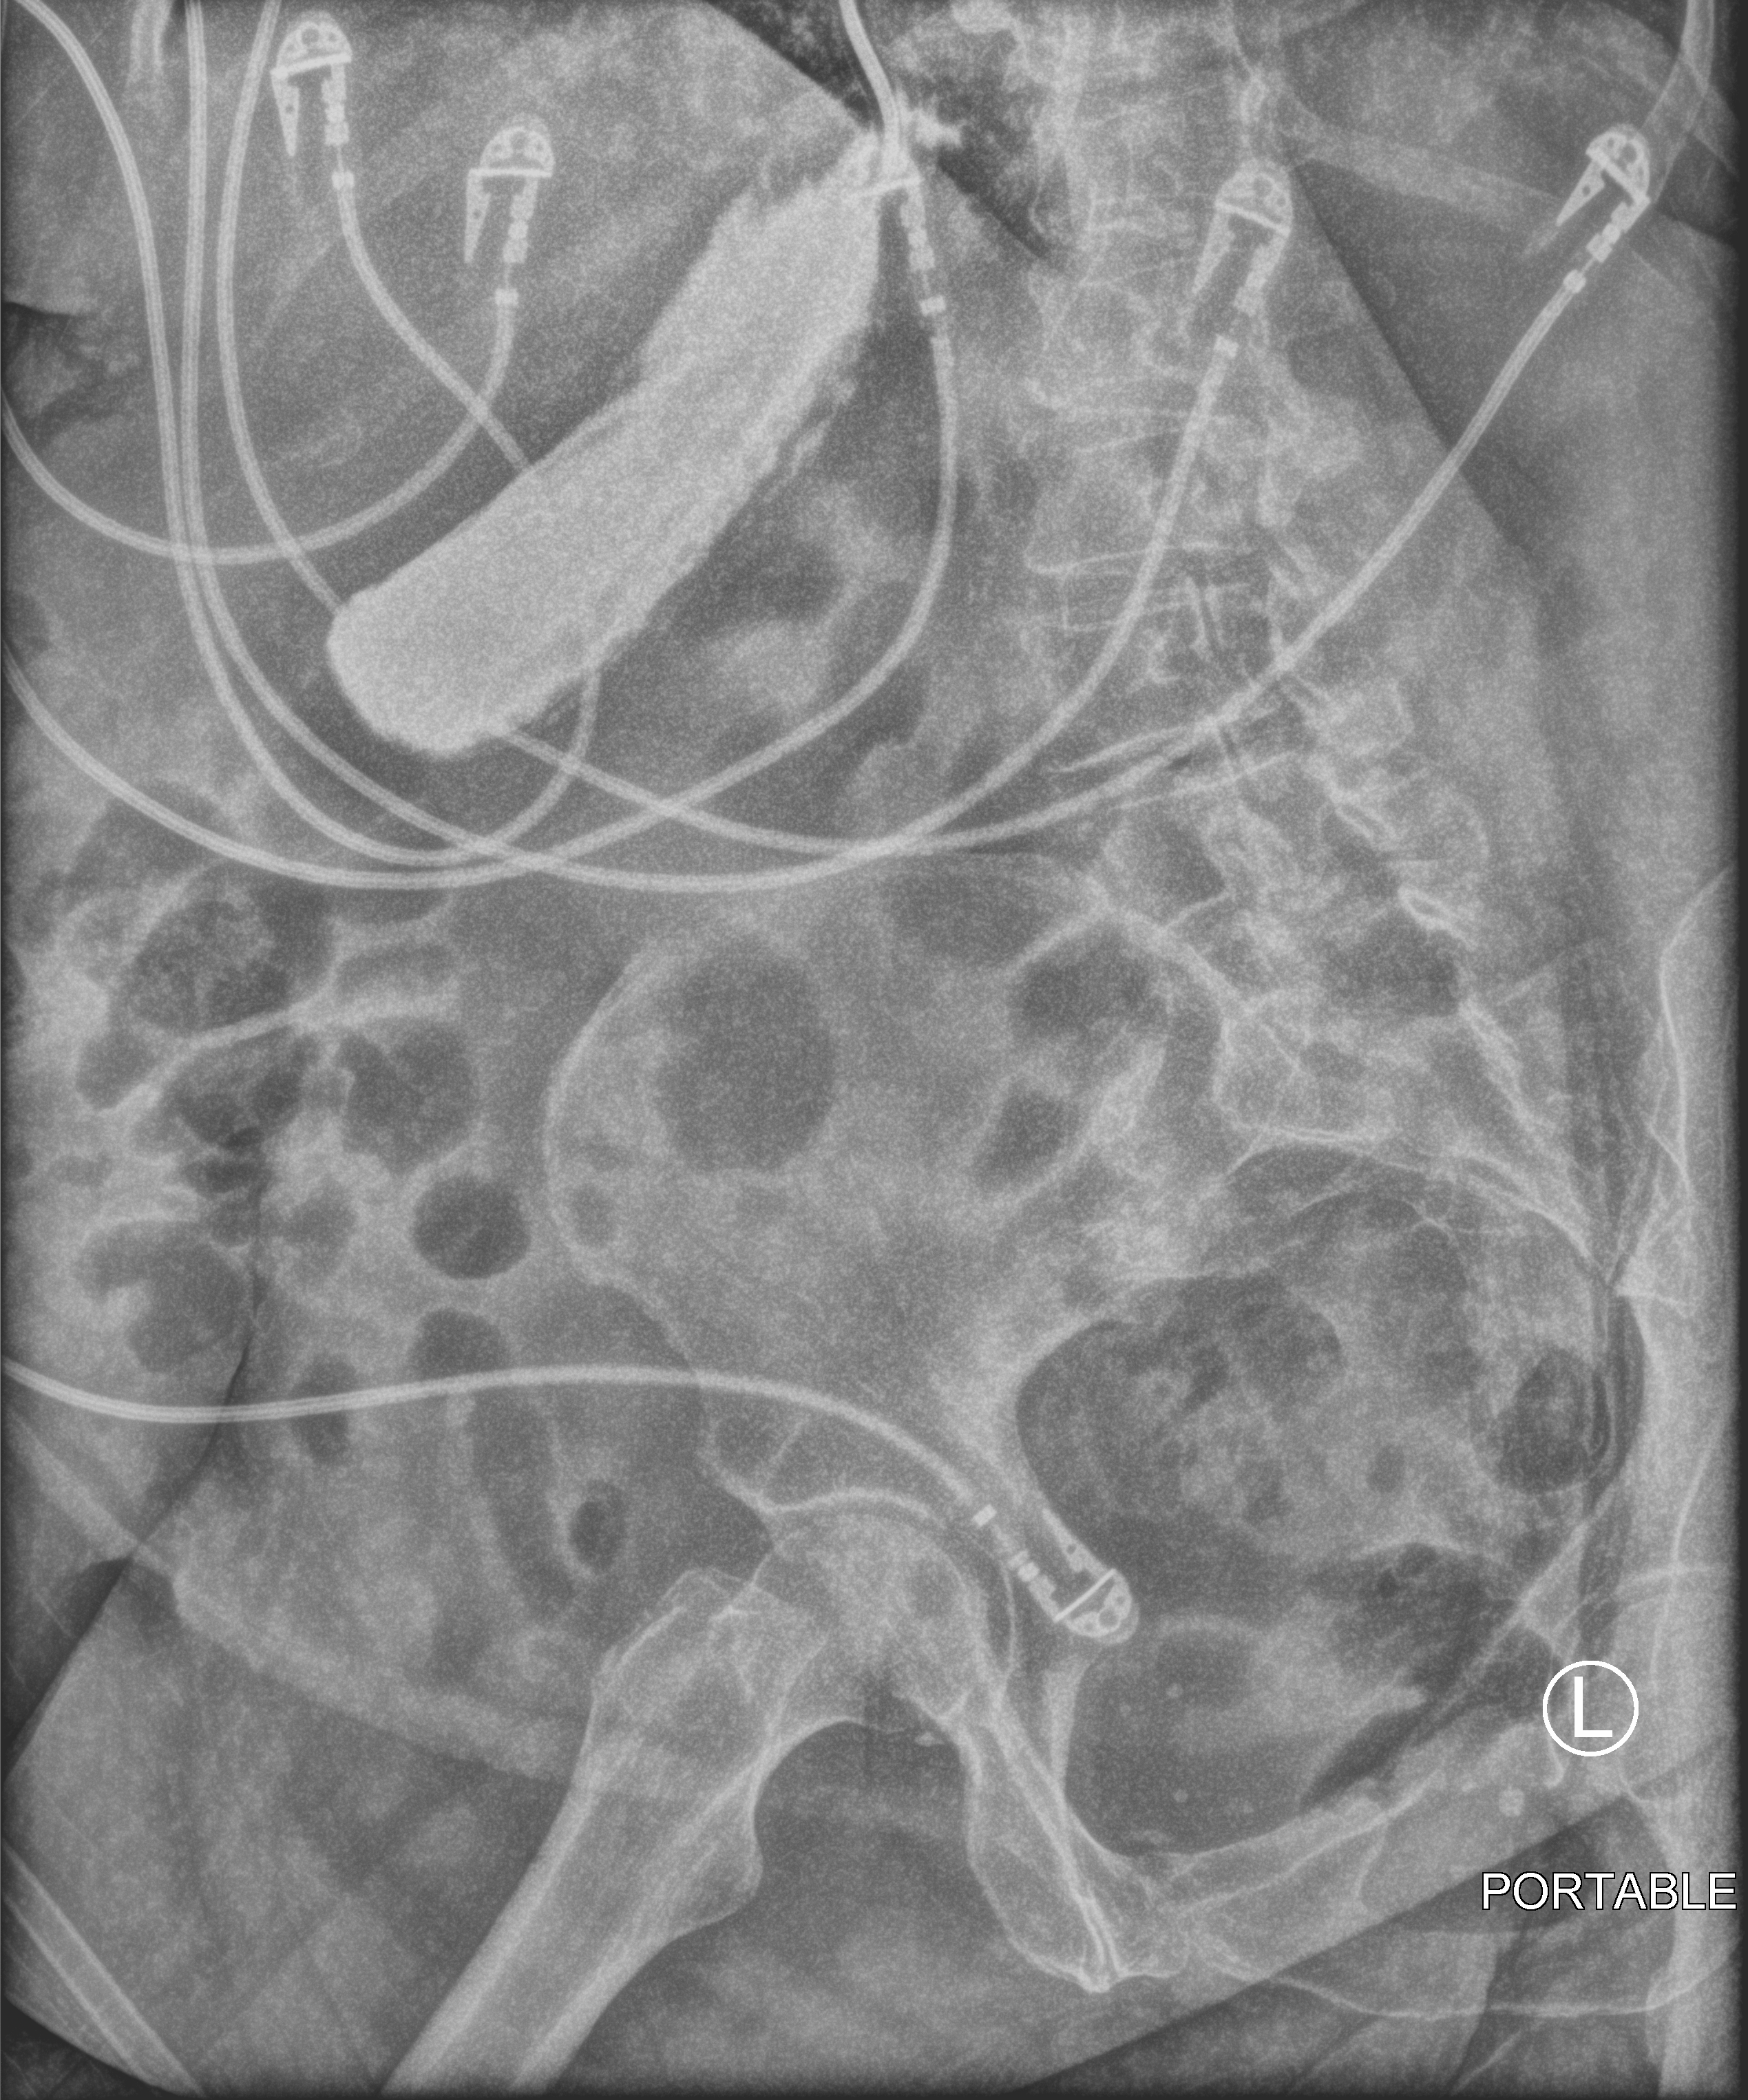
Bedside abdomen radiograph (computed radiography); anteroposterior (AP) projection. Patient hospitalised with COVID-19; female, aged 75–90 years.
Hospital-stay facts (about this admission, not read from this image; timing relative to this image not recorded): admitted to intensive care during this hospital stay: yes; mechanically ventilated during this hospital stay: yes.